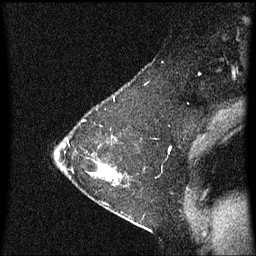
Breast MRI (dynamic contrast-enhanced), one sagittal slice; dynamic contrast-enhanced series, image 2 of 3 at this slice position (ordered by acquisition); 1.5 T; TE 4.2 ms, TR 8.4 ms; 2 mm slice thickness; 256 × 256 image matrix. Female patient, age 36 years. Case-level facts recorded for this patient, not image findings: setting: breast cancer imaged before/during neoadjuvant chemotherapy; receptor status: HR-positive, HER2-negative.
Structures marked on this image (semi-automatically segmented with operator editing):
- analysis volume of interest (the breast-tissue region the enhancement analysis was run in; not a lesion): box from (x=72, y=118) to (x=123, y=187) px
- tumour enhancement mask (voxels above the 70 % enhancement threshold inside the analysis volume of interest): (x=90, y=164)–(x=121, y=181)